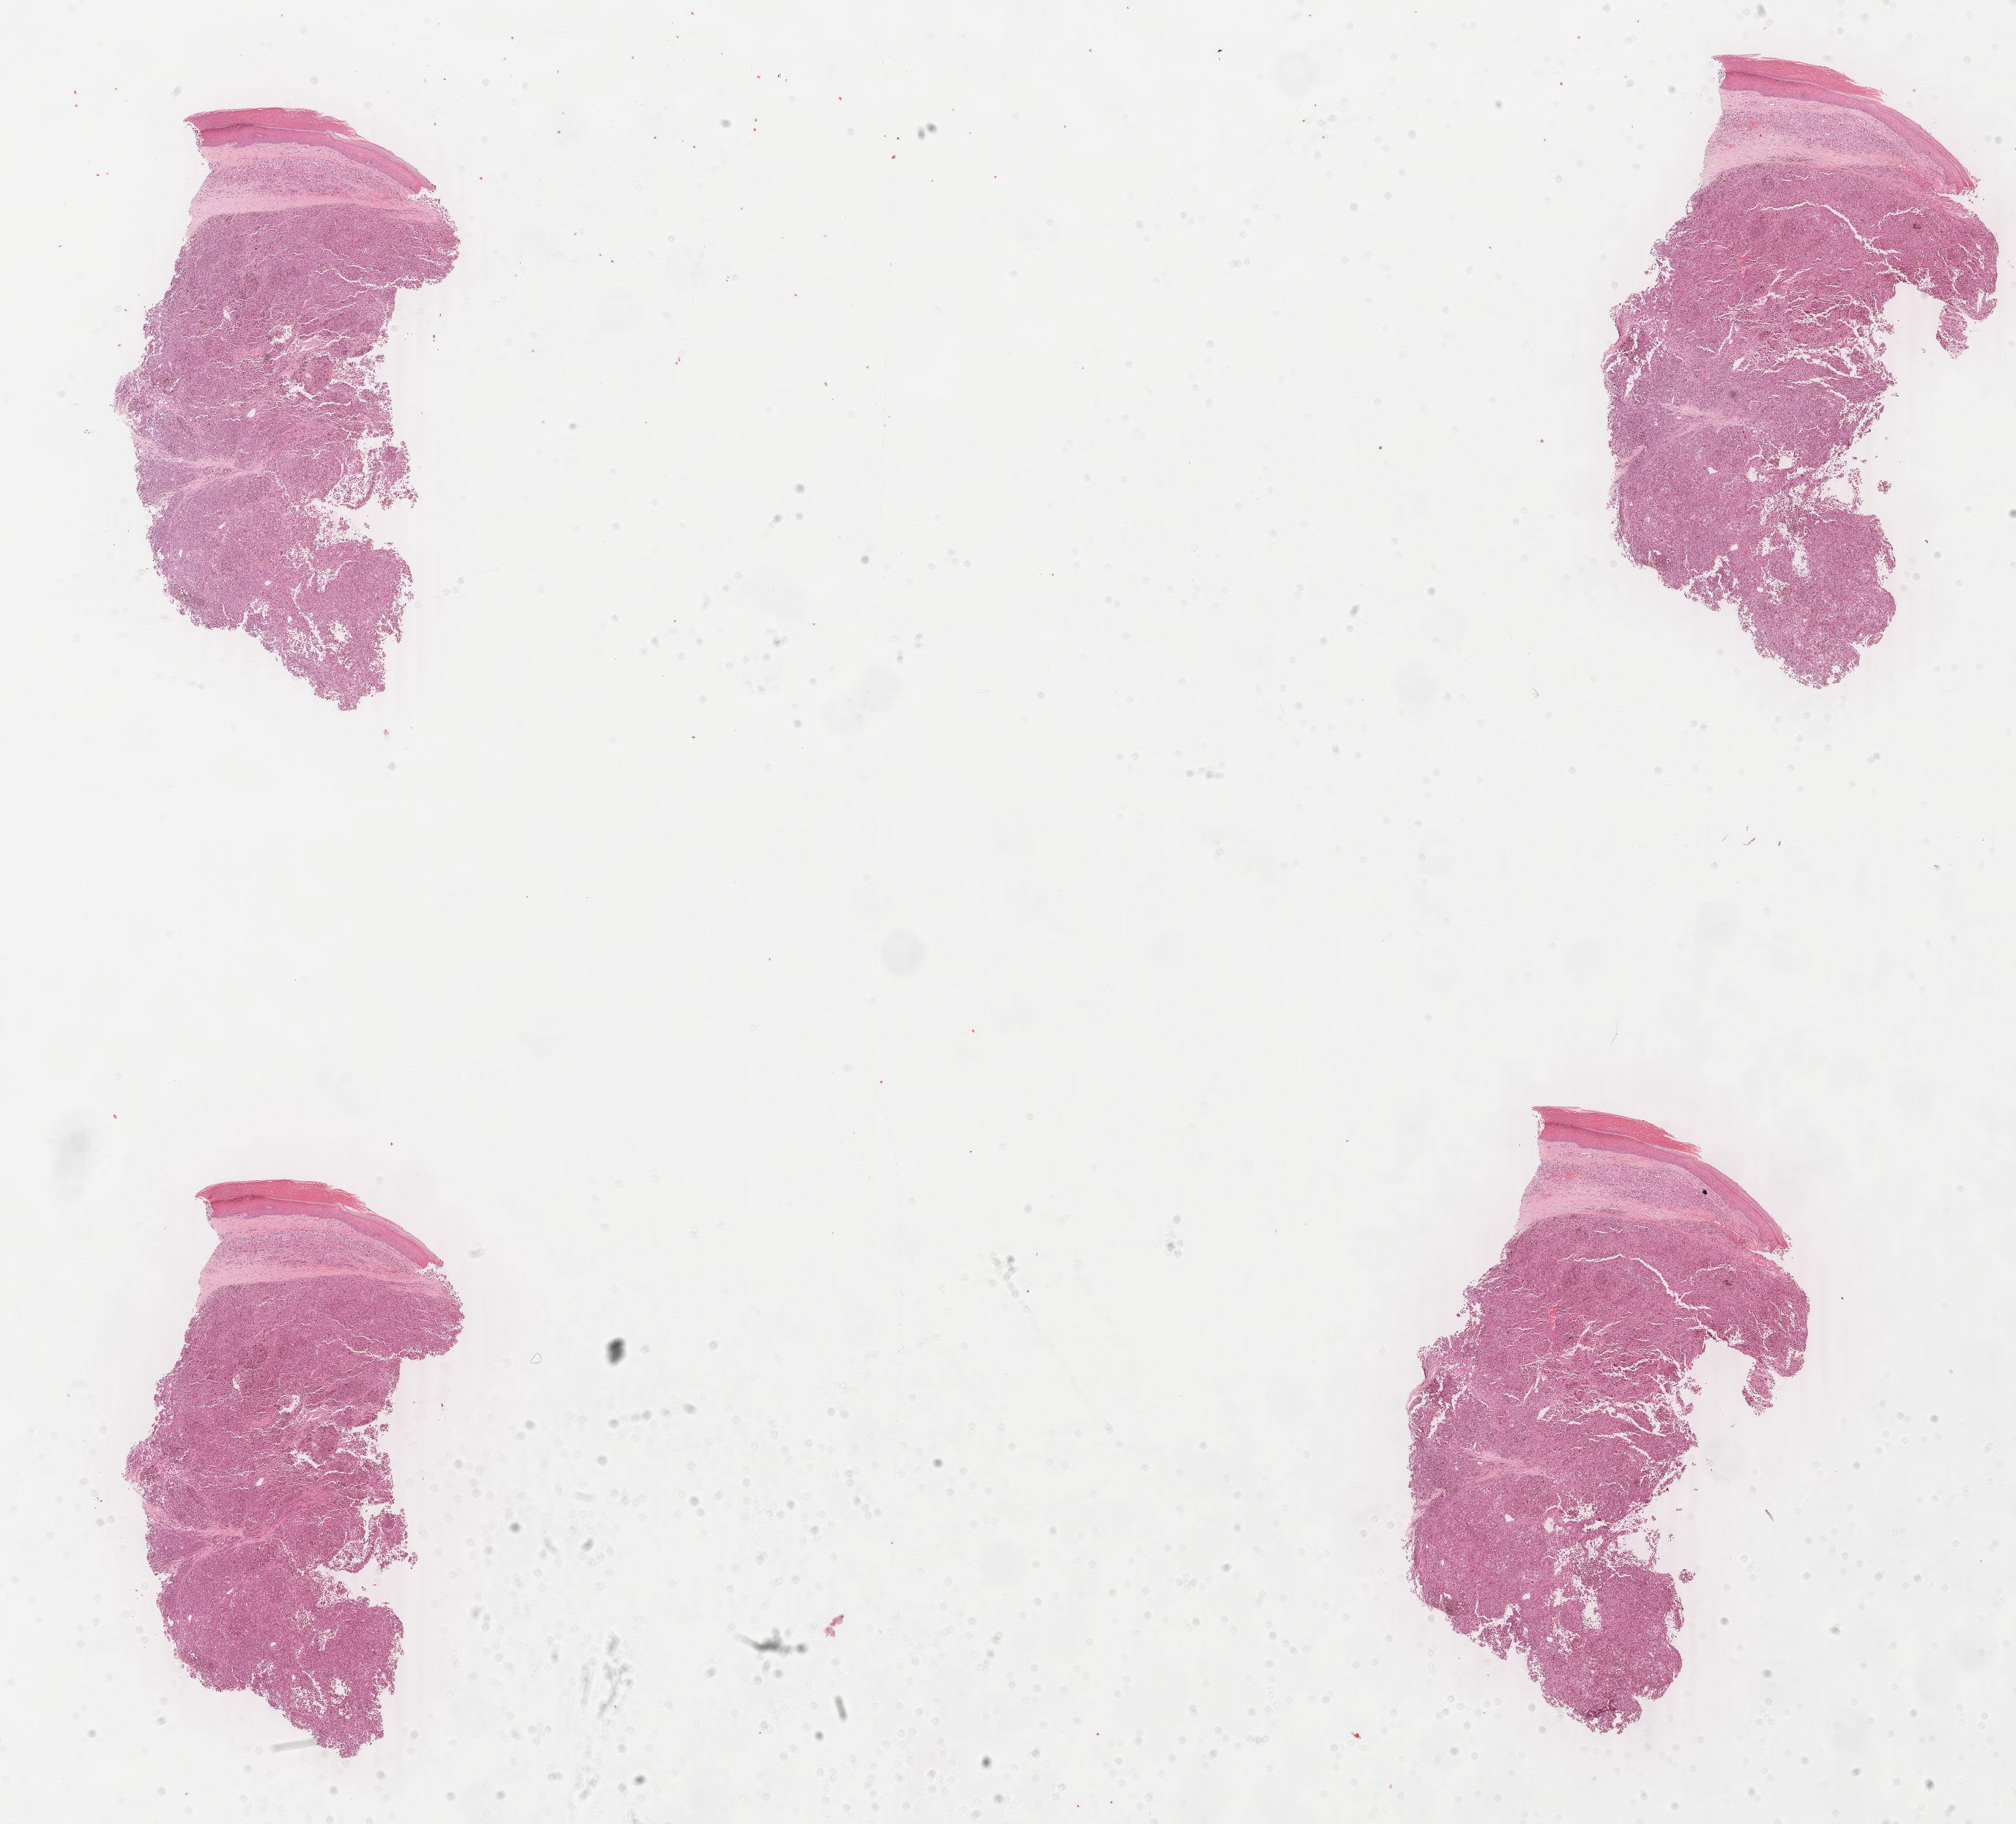
Digitized Hematoxylin and eosin (H&E) stained tissue section (whole slide) — low-resolution overview of the scanned area, about 21.9 x 19.8 mm (acquisition: 40x scan); FFPE section; skin, primary tumour sample. Patient: female, age at initial diagnosis 56 years.
Histologic diagnosis: Malignant melanoma, NOS.